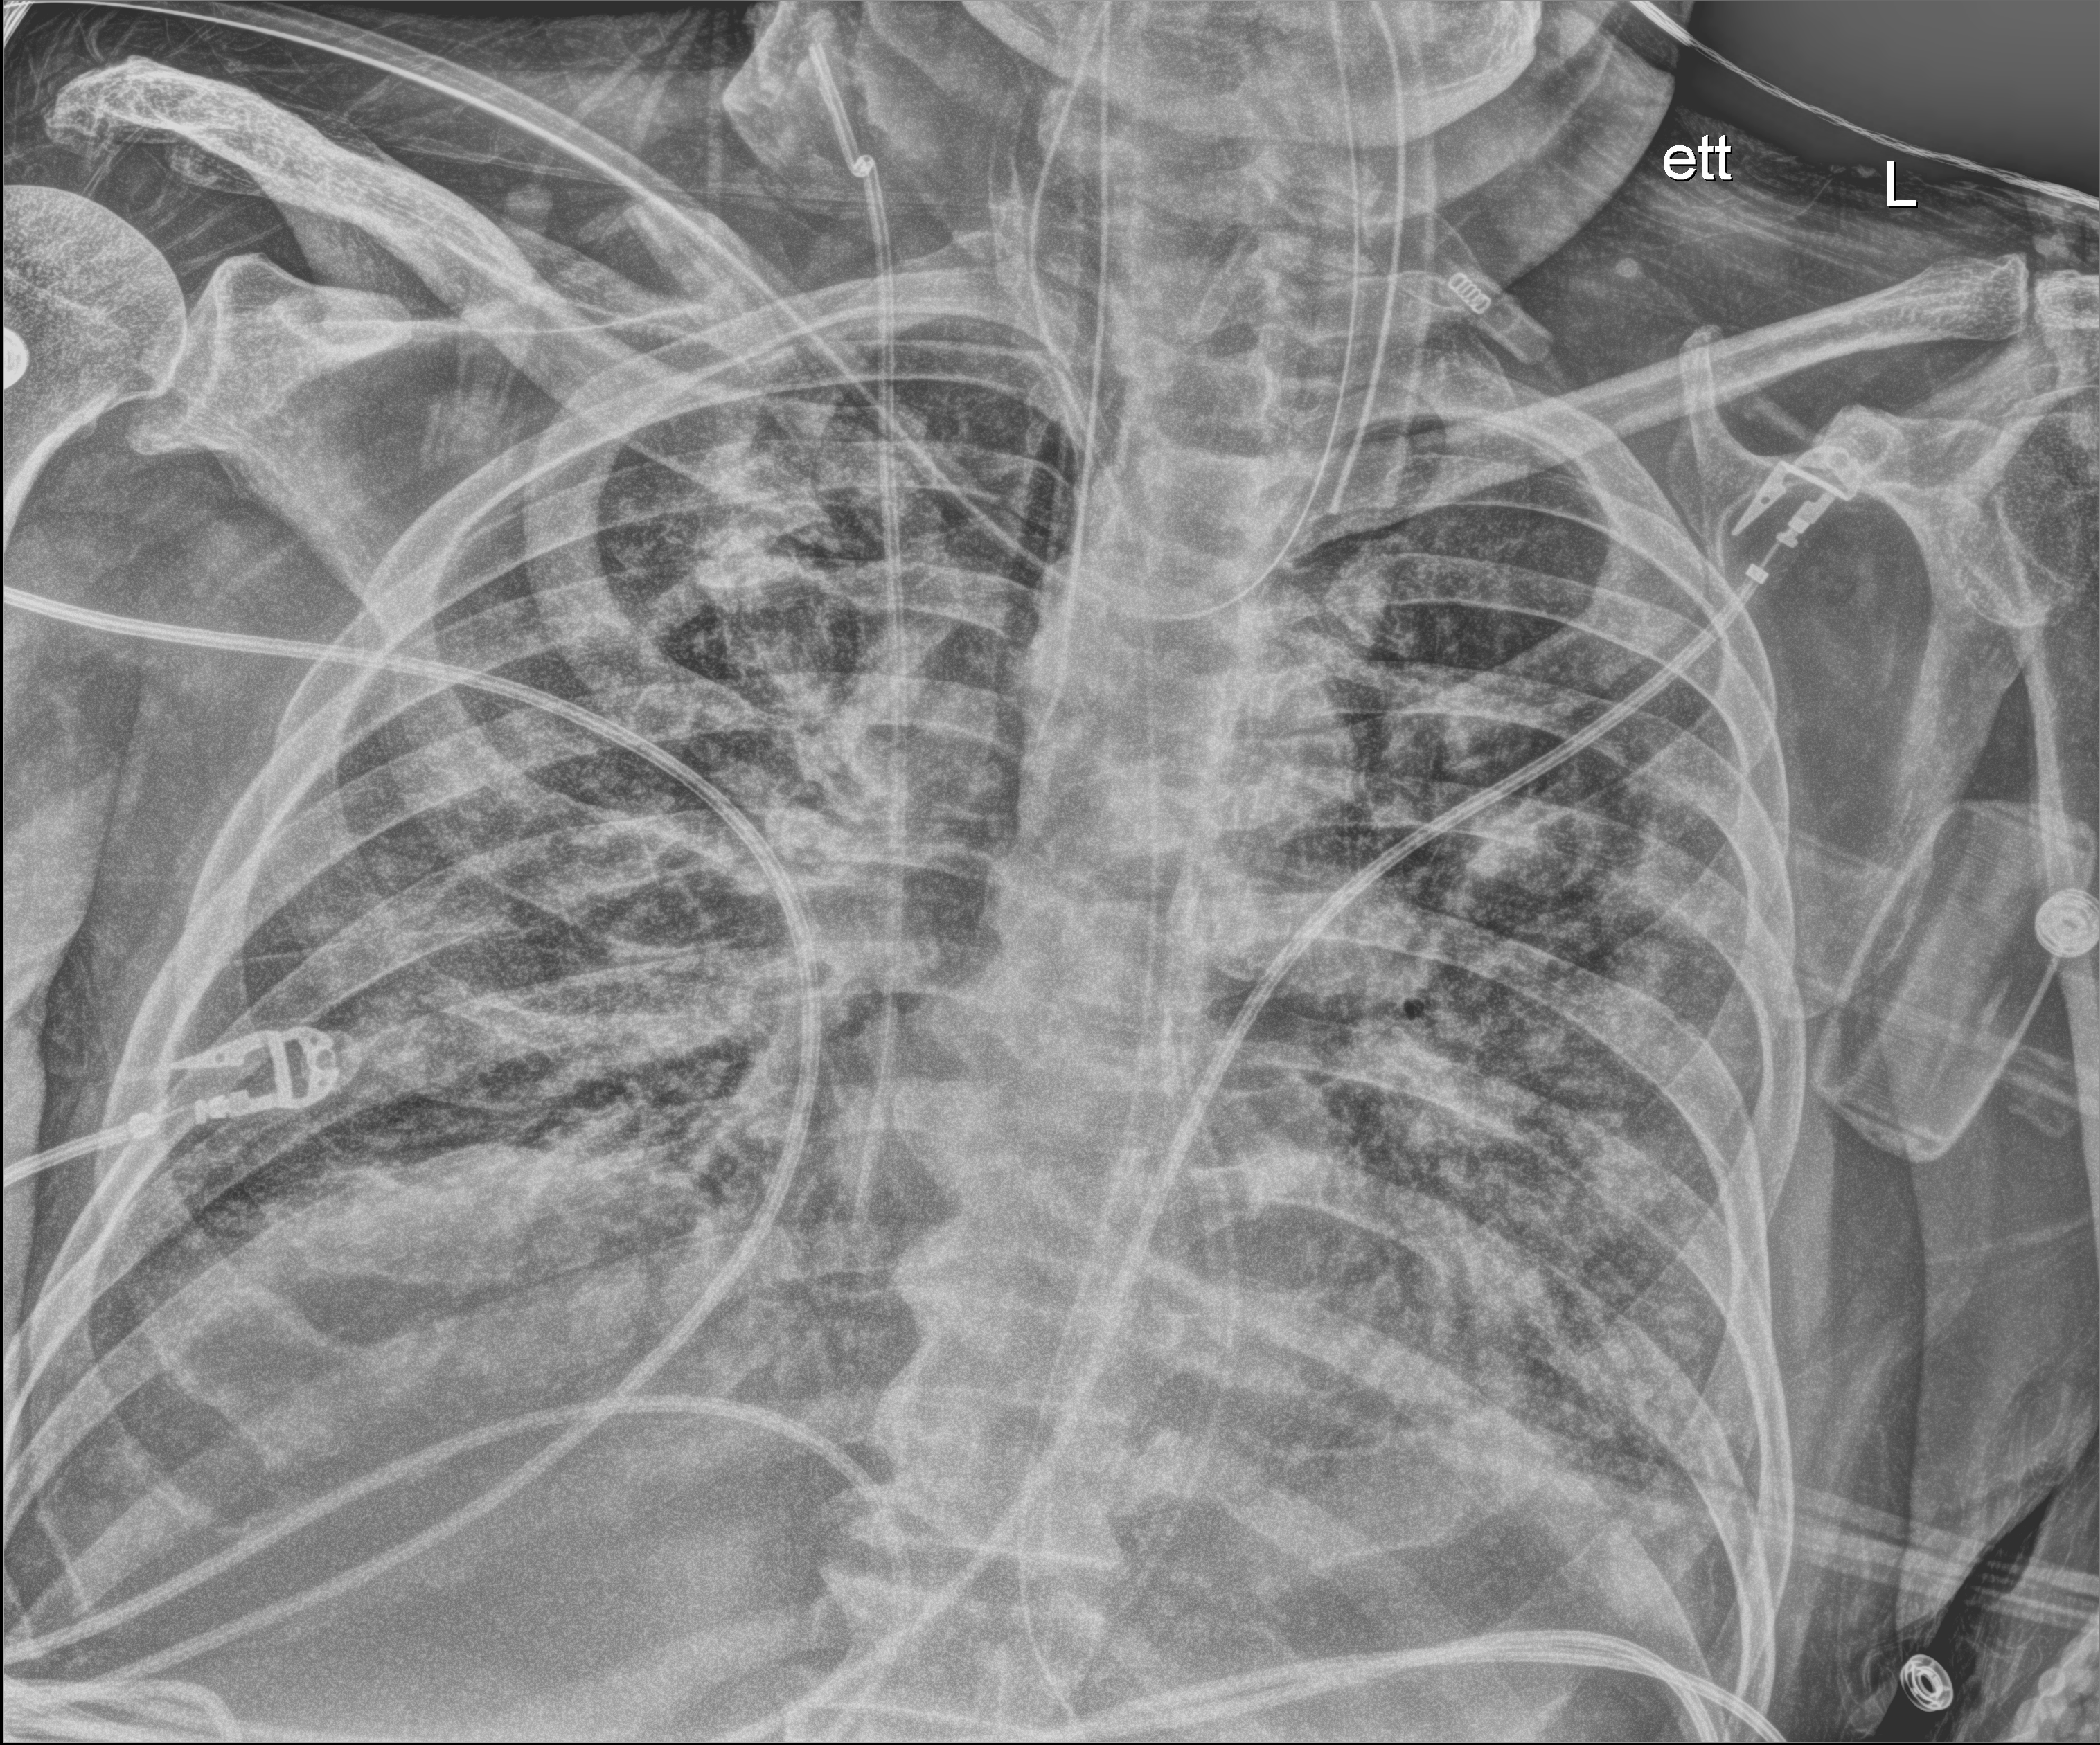
Portable chest radiograph; anteroposterior (AP) projection. Male patient hospitalised with COVID-19, age 75–90 years.
From the hospital-stay record, not from the radiograph (when in the stay this image was taken is not recorded): admitted to intensive care during this hospital stay: yes; mechanically ventilated during this hospital stay: yes; length of hospital stay: 33 days.